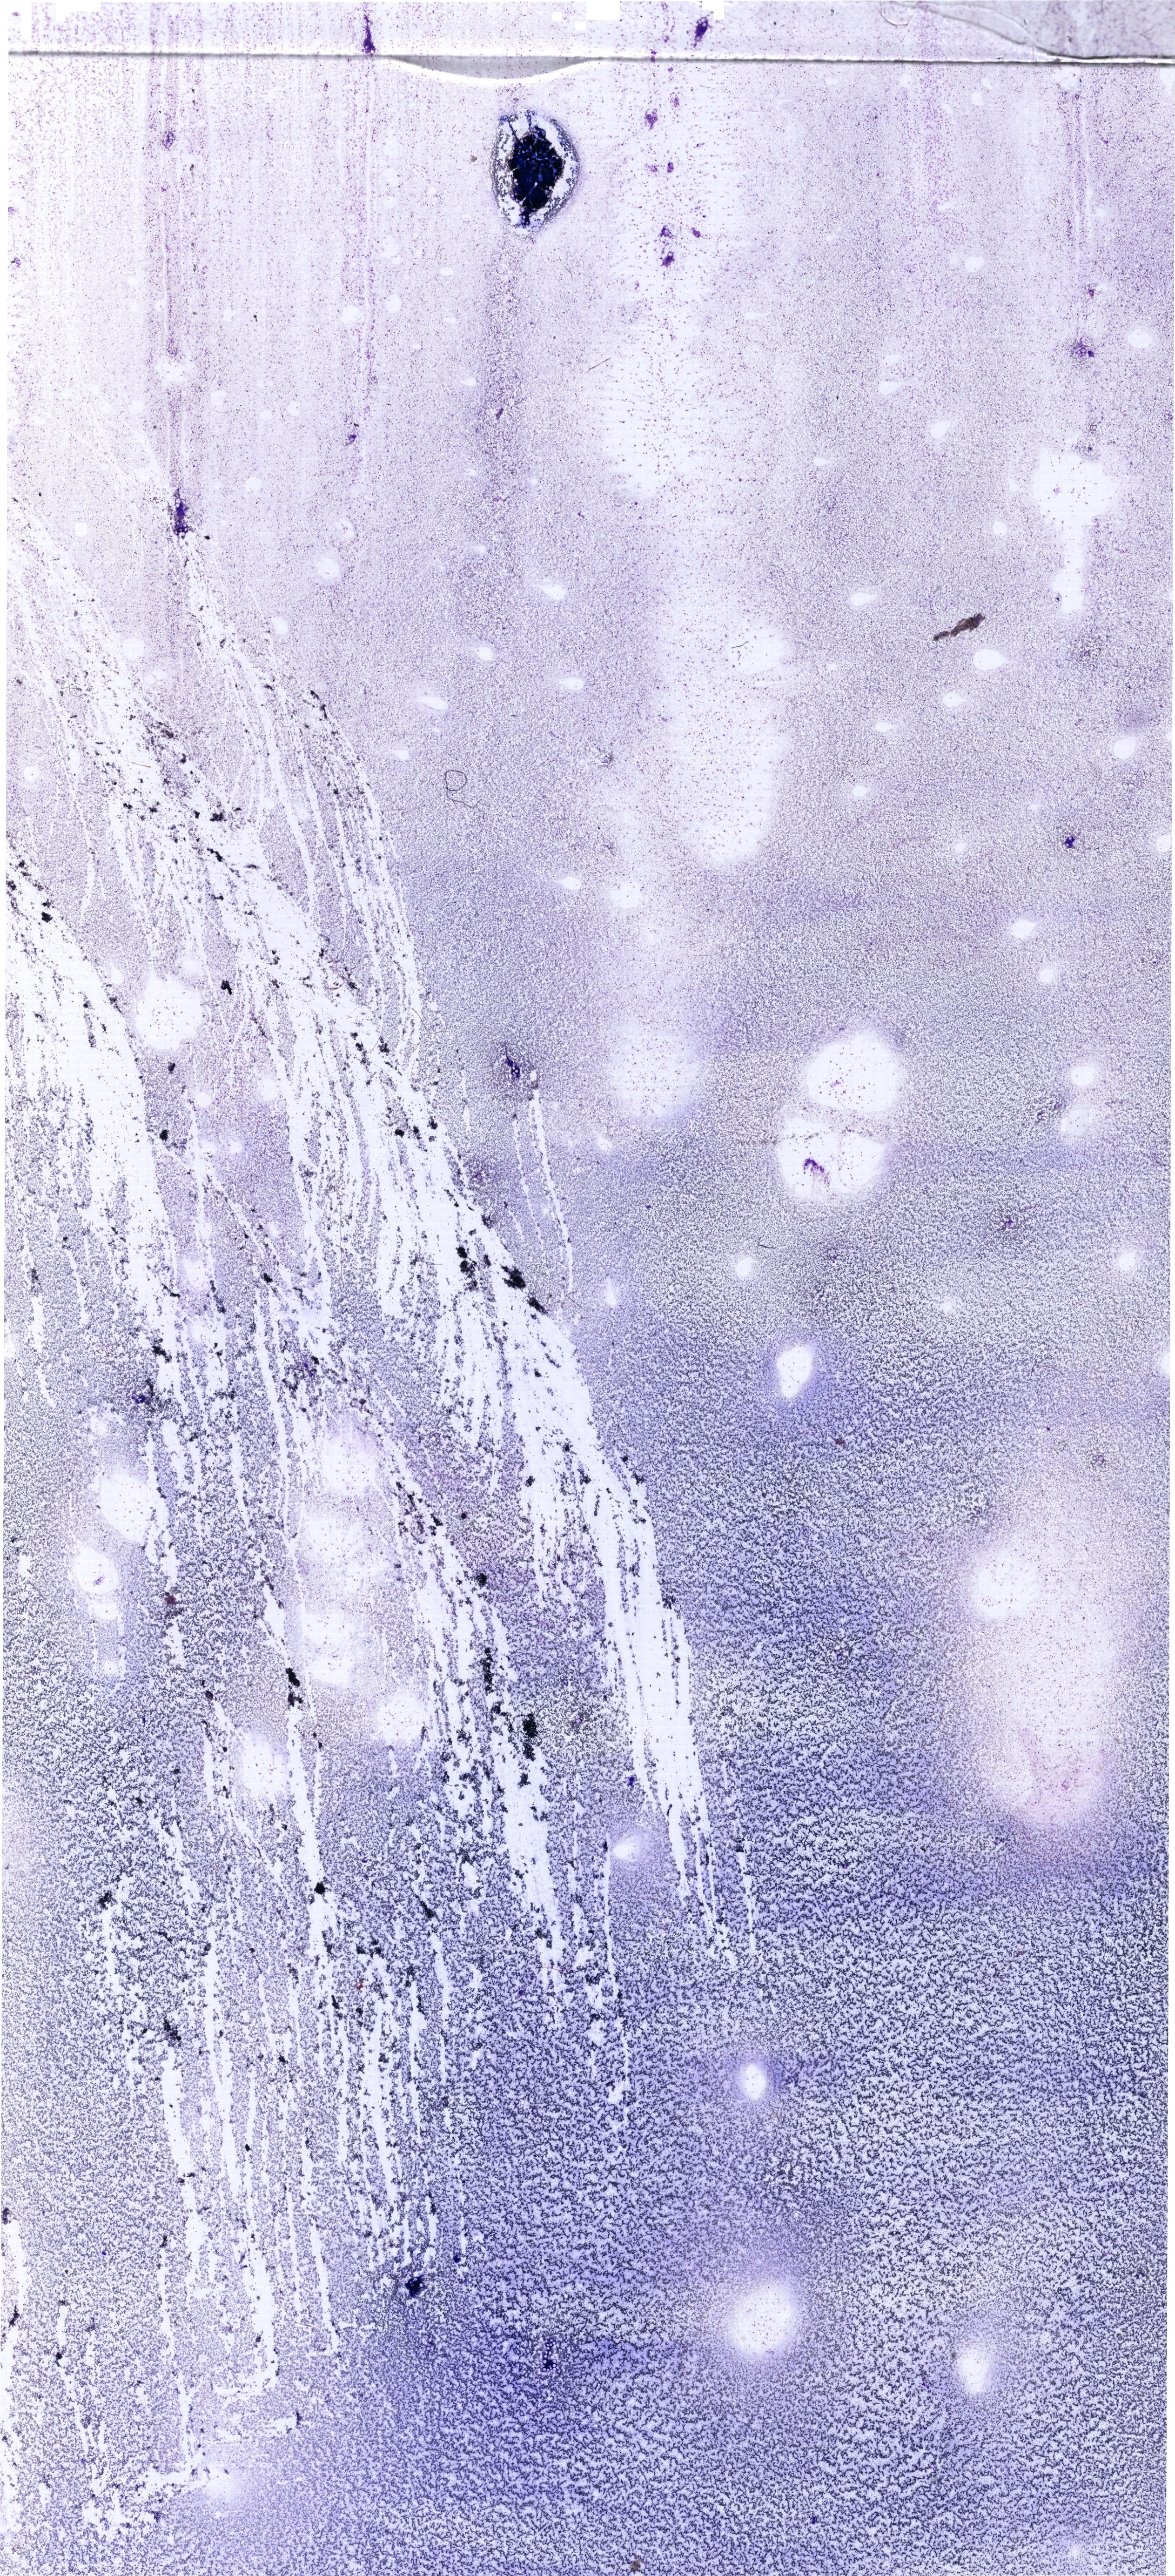
Bone marrow aspirate smear, May-Grünwald-Giemsa (MGG) stain, whole-slide image — shown as a low-resolution overview of the whole scanned area (about 19.7 x 43.2 mm). Patient sex: female.
Diagnosis: Mixed Phenotype Acute Leukemia, B/Myeloid.